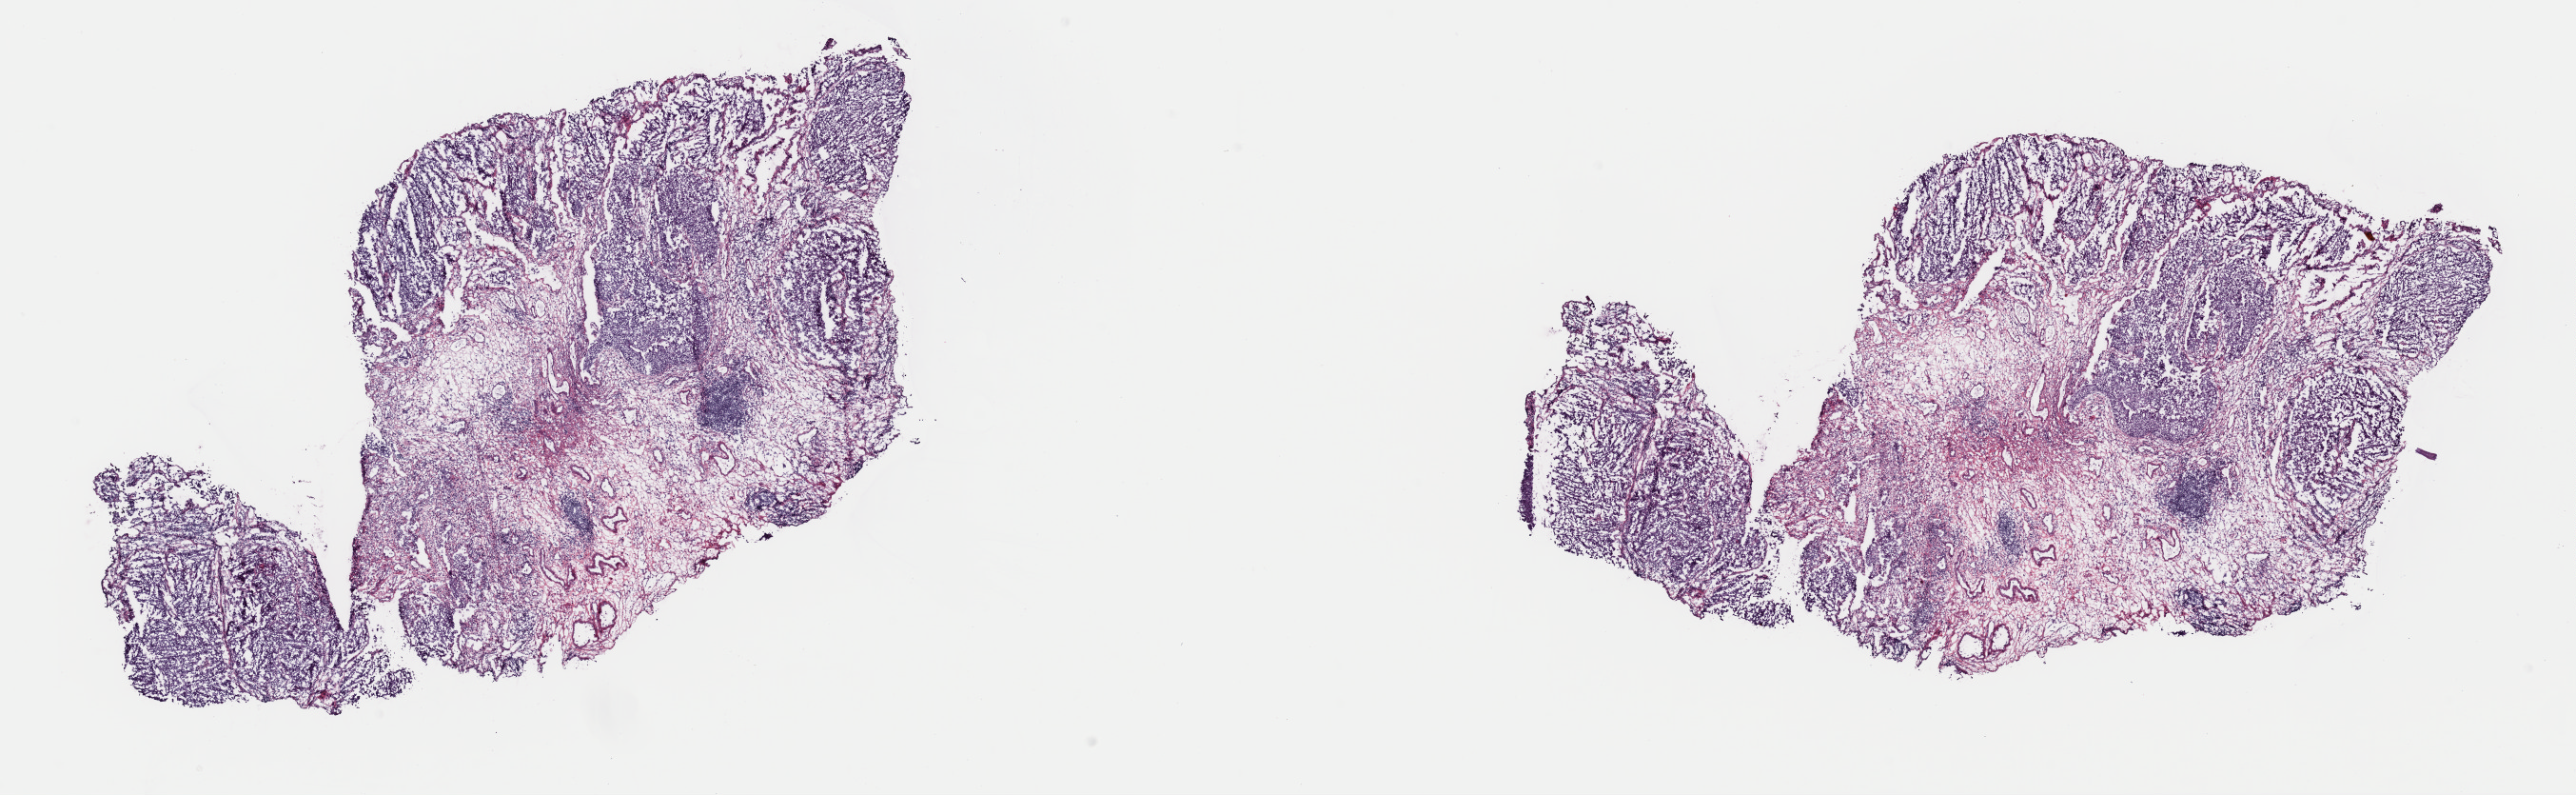
Whole-slide histology image, Hematoxylin and eosin (H&E) stained, shown as a low-resolution overview of the whole scanned area (about 21.4 x 6.6 mm, from a 40x scan); frozen section; bladder, primary tumour sample. Female patient; age at initial diagnosis 56 years. Histologic grade: high grade. Composition of this section per pathologist review: tumour cells 100%, tumour nuclei 85%, normal cells 0%, stromal cells 0%, necrosis 0%. Infiltration values recorded for this section: lymphocyte infiltration 2%, monocyte infiltration 0%, neutrophil infiltration 0%.
* AJCC pathologic stage: IV (7th edition)
* TNM: T4a N2 M0
* pathologic diagnosis: Transitional cell carcinoma
* lymph nodes positive (case pathology): 5 of 37 examined